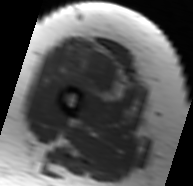
MRI of an extremity soft-tissue mass, one axial slice. Position 24 of 91 along the scan axis. MR volume resampled by the dataset authors to the PET/CT grid (not the native acquisition matrix). 3.27 mm slice thickness. 193 × 186 image matrix, field of view 188 × 182 mm. Female patient. From the clinical record (not read from this slice): histological type: malignant solitary fibrous tumor; grade: intermediate; site of the primary tumour: right thigh.
Annotated regions visible in this slice (expert contour drawn on MRI and transferred to this co-registered scan by the dataset authors):
- gross tumour volume including surrounding oedema: box from (x=51, y=37) to (x=144, y=107) px
- gross tumour volume (mass): (x=60, y=51)–(x=121, y=95)